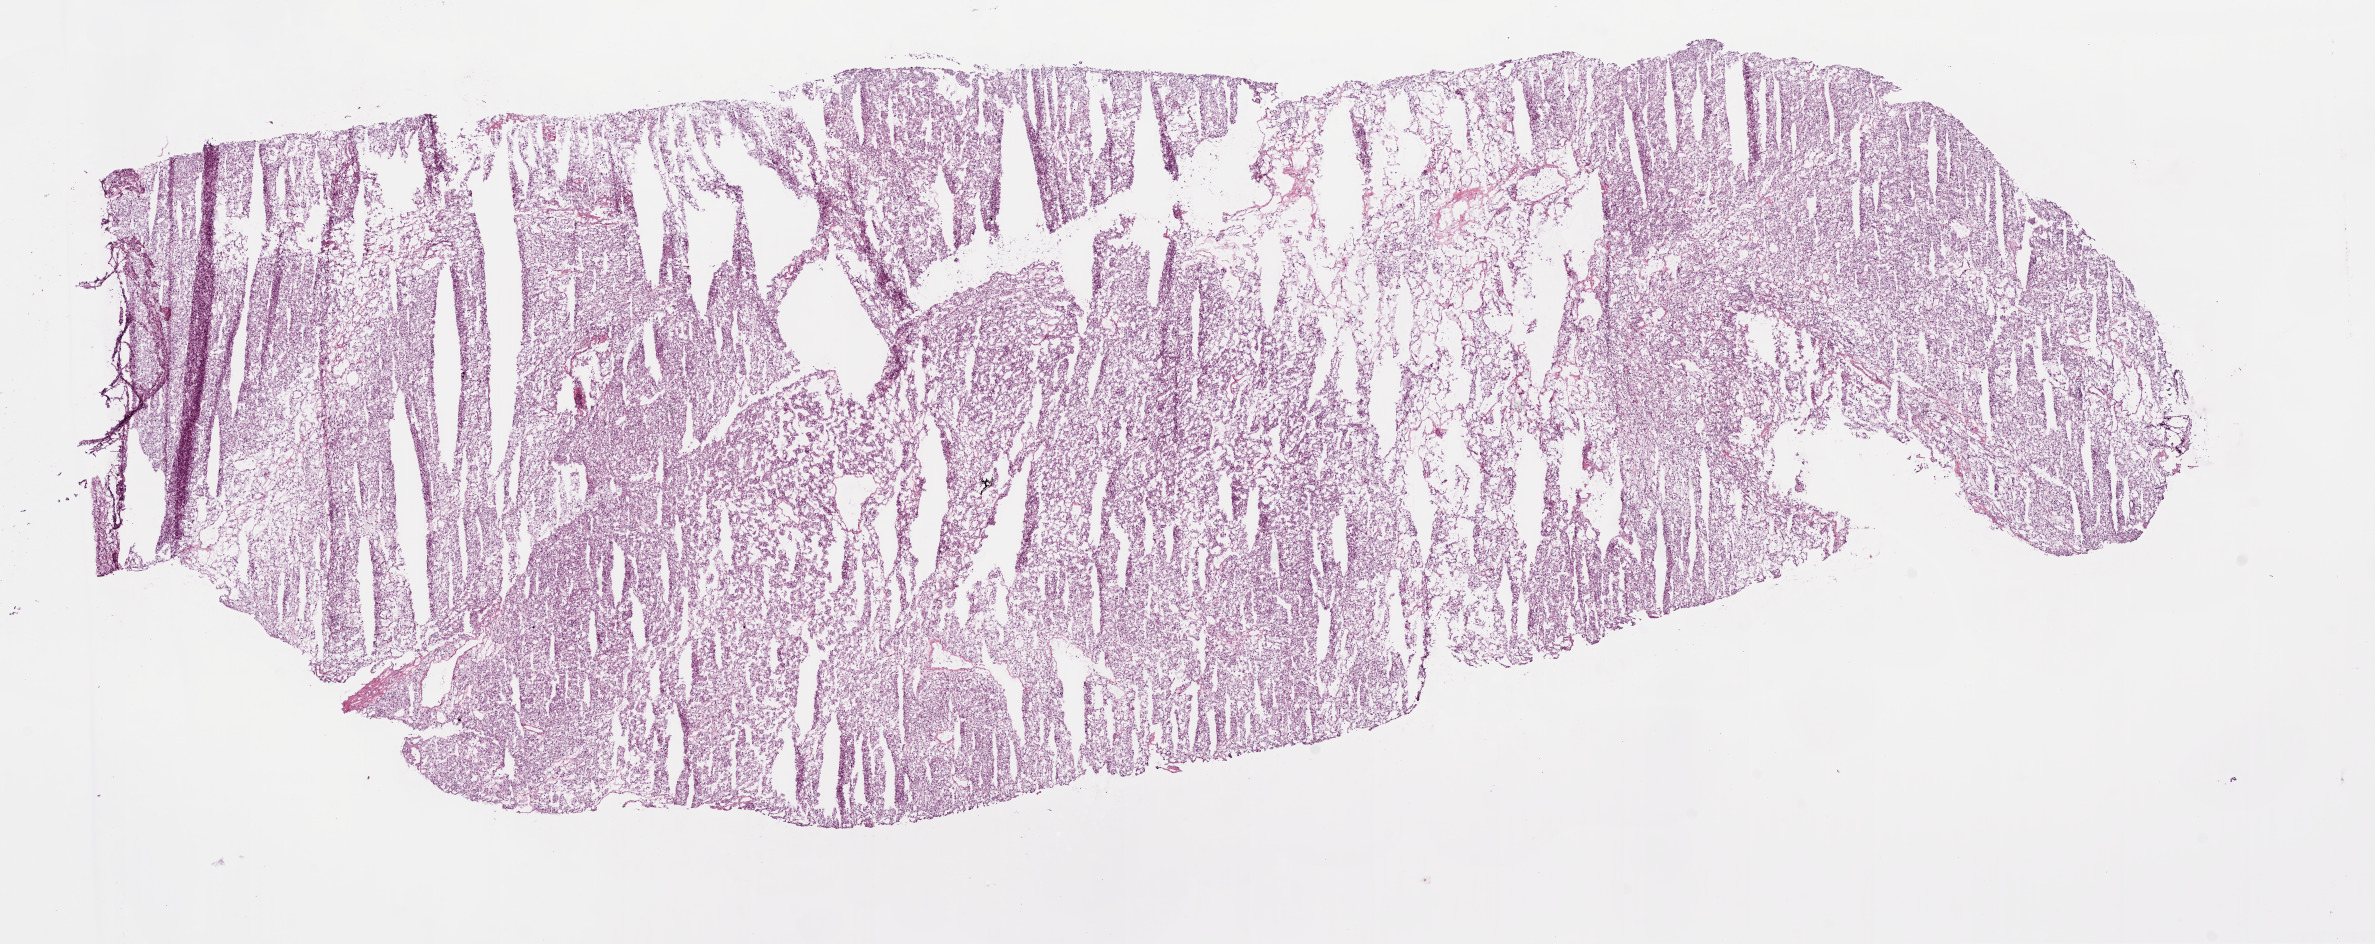
H&E whole-slide image, shown as a low-resolution overview of the whole scanned area (about 19.1 x 7.6 mm, from a 20x scan); frozen section; kidney, primary tumour sample. Patient: female, age at initial diagnosis 78 years. Histologic grade: G2 (moderately differentiated). Pathologist review of this section (percent, as recorded): tumour cells 95%, tumour nuclei 90%, normal cells 0%, stromal cells 5%, necrosis 0%.
- AJCC pathologic stage: I
- laterality: left
- pathologic diagnosis: Clear cell adenocarcinoma, NOS